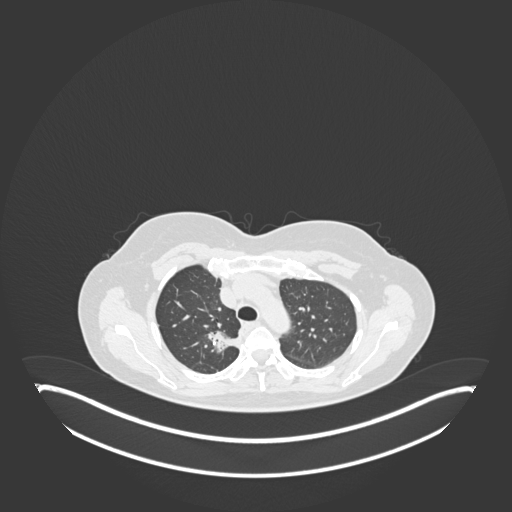
Chest CT, one axial slice; slice 135 of 181 in the series (ordered by position); reconstruction kernel B30f; 120 kVp; lung window (W 1500 / L -600 HU); 512 × 512 image matrix. Female patient, age 65 years. Case-level facts recorded for this patient, not image findings: clinical TNM (as recorded): T1b N0 M0; histopathological grade: G2.
Structures marked on this image (bounding box drawn by a radiologist):
- lung tumour (recorded histology: adenocarcinoma): bounding box [x1, y1, x2, y2] px = [206, 330, 243, 354]